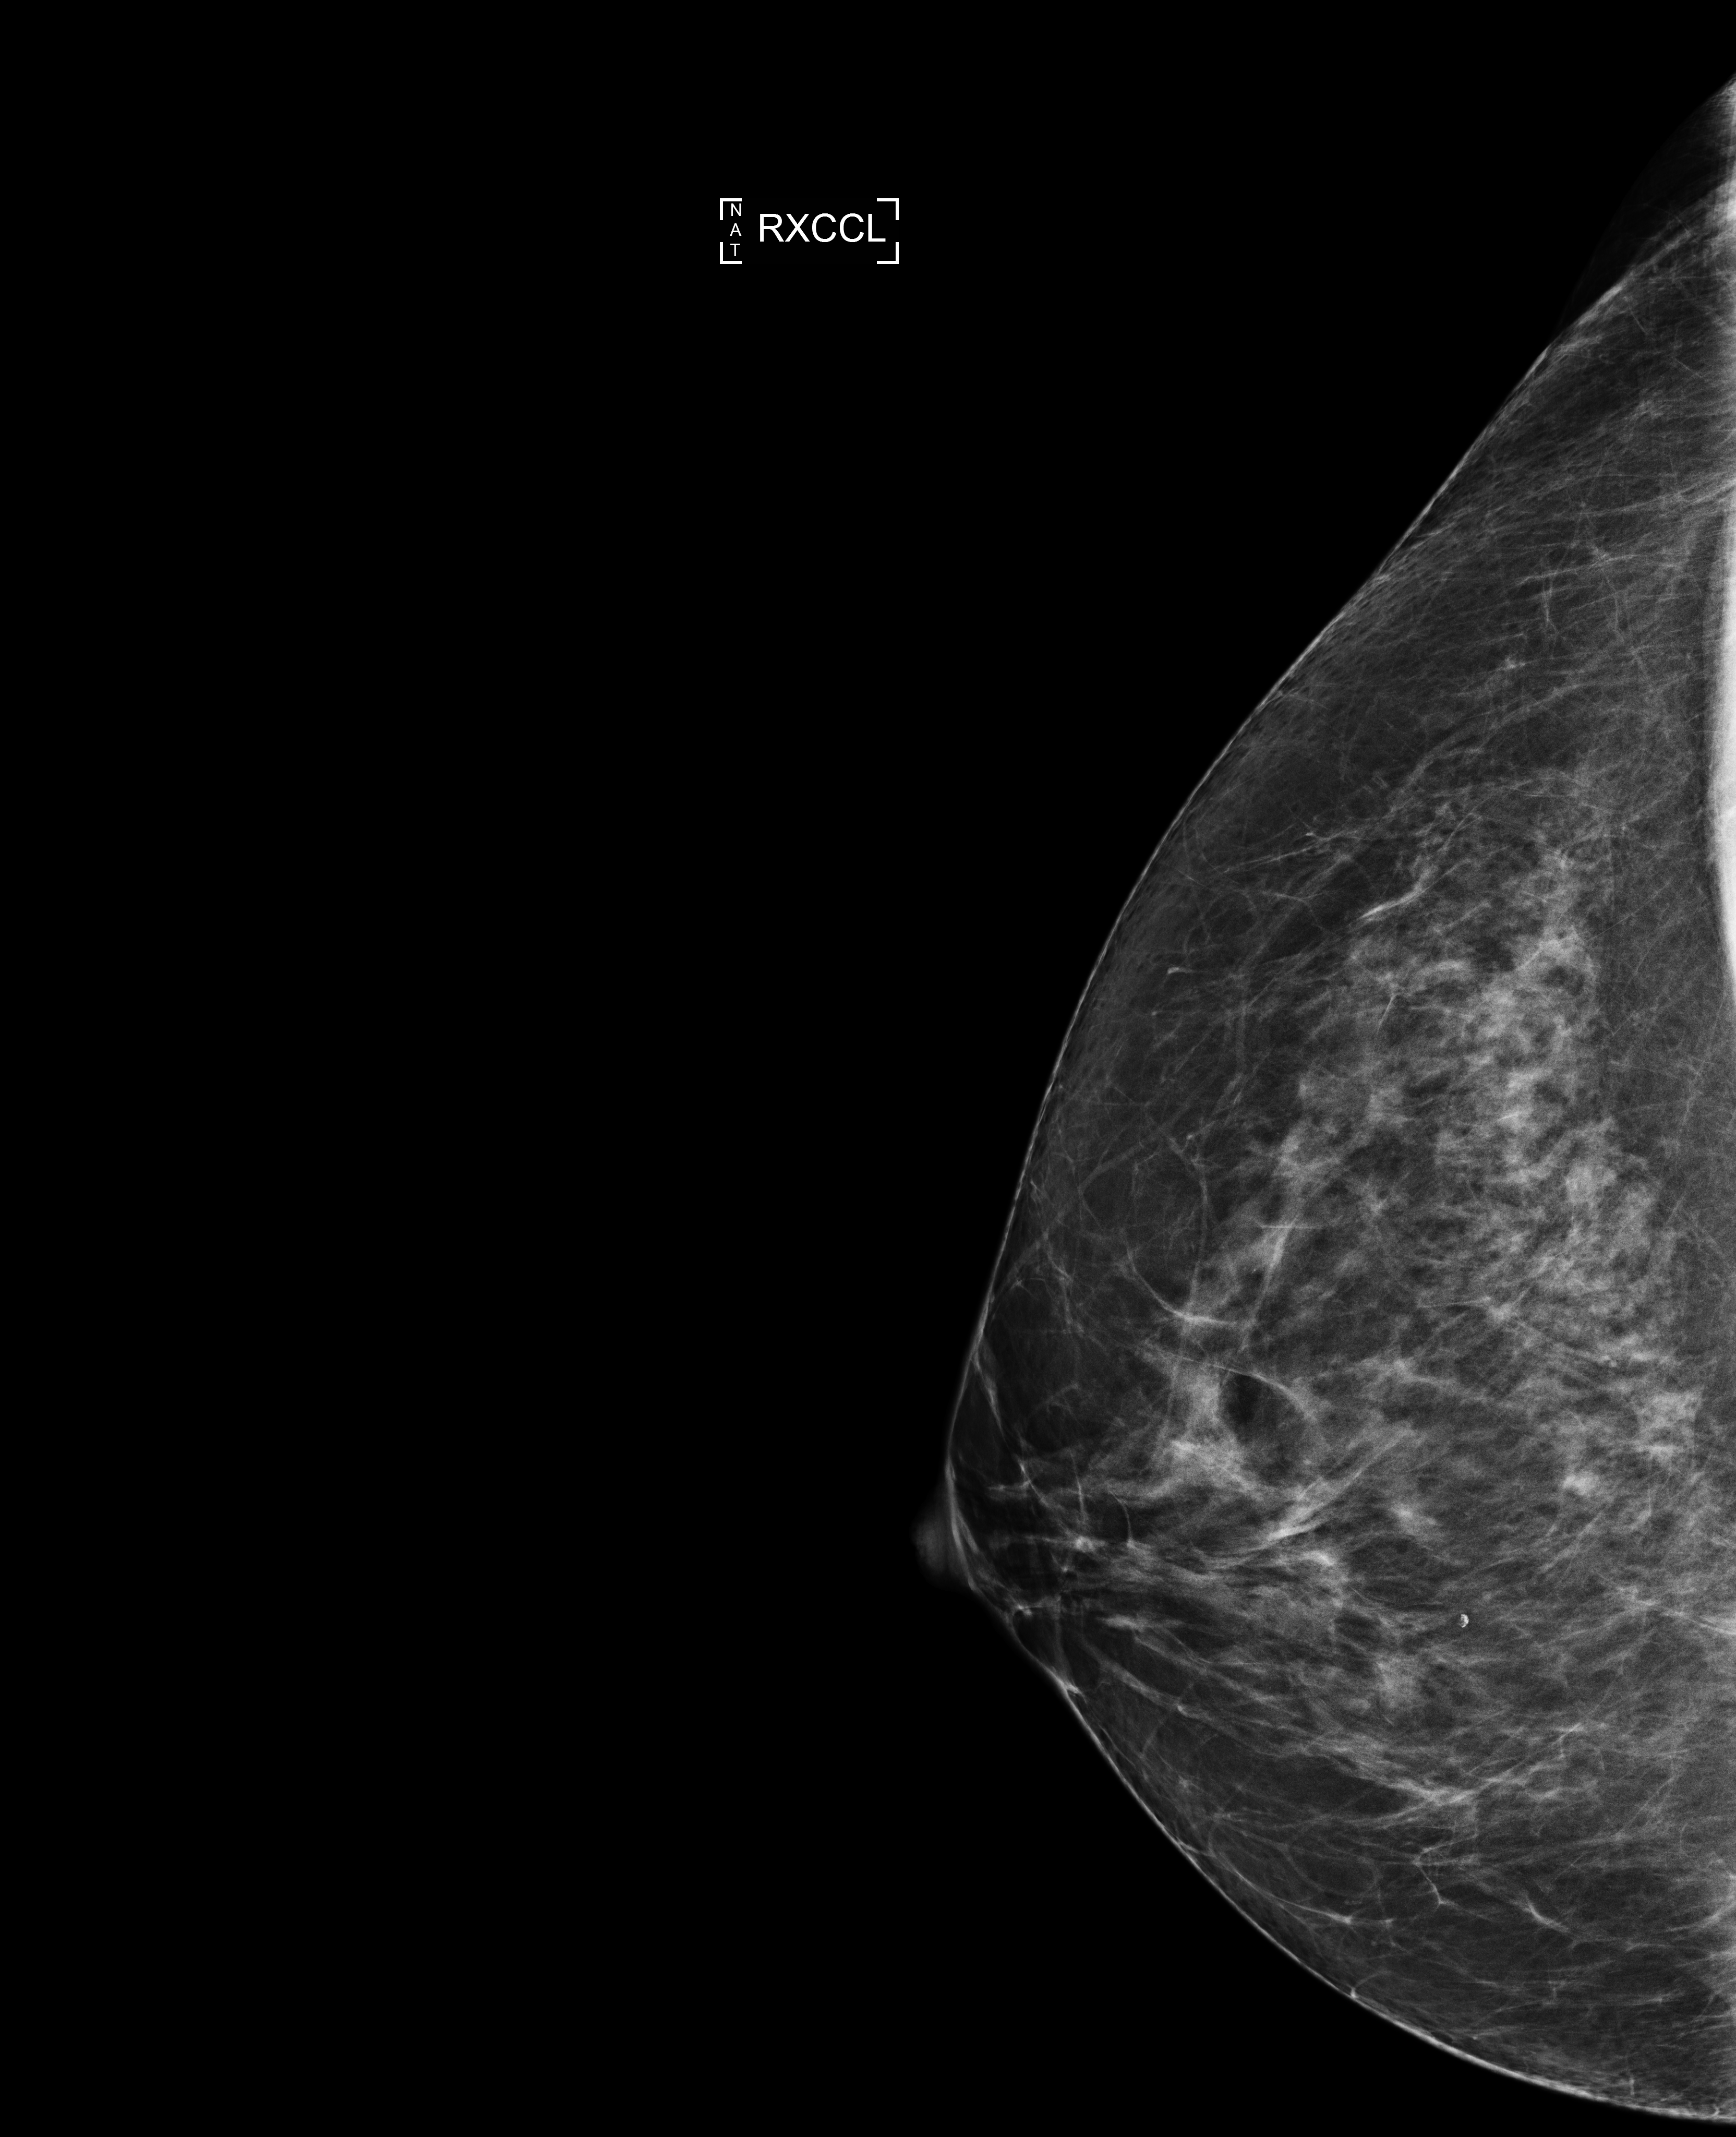
Screening examination; system: Selenia Dimensions. Patient: female, 52 years.
Image type: full-field digital mammogram. Breast: right. Projection: exaggerated CC view (lateral).